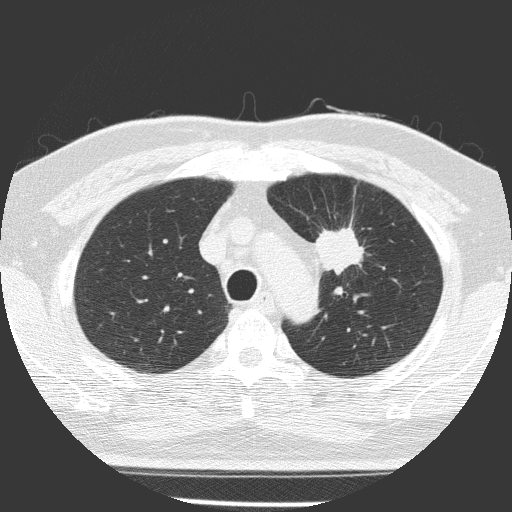
Axial slice from a low-dose chest CT screening exam; baseline annual screen; lung window (W 1500 / L -600 HU); lung (sharp) reconstruction kernel (FC51); slice 40 of 156 in the series. Male, age 70 years at enrolment. Current smoker at enrolment.
- Expert-annotated lung lesion, bounding box <297,220,372,294> (left, top, right, bottom; pixels).
- The screening reader recorded 3 non-calcified nodules or masses ≥4 mm on this exam (left upper lobe, left lower lobe, left upper lobe); which of them this box marks is not recorded.
- Participant outcome: lung cancer diagnosed 58 days after this screen — squamous cell carcinoma, NOS, left upper lobe, poorly differentiated (G3), stage IB (AJCC 6th edition), 47 mm at pathology.